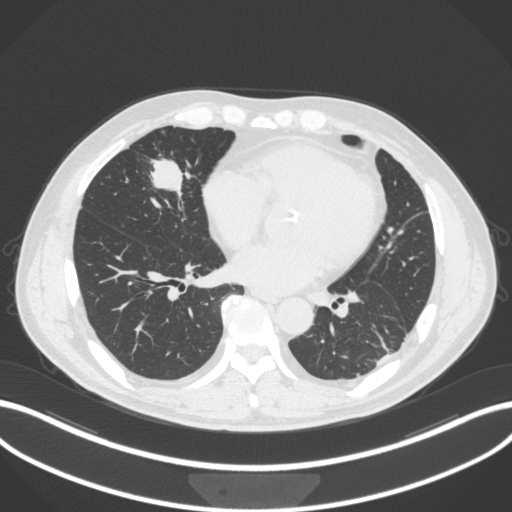
Chest CT, one axial slice; position 112 of 399 along the scan axis; 120 kVp; lung window (W 1500 / L -600 HU); 512 × 512 image matrix, field of view 400 × 400 mm. Male patient, age 59 years. Case-level facts recorded for this patient, not image findings: clinical TNM (as recorded): T2a N1 M0.
Structures marked on this image (bounding box drawn by a radiologist):
- lung tumour (recorded histology: adenocarcinoma): bounding box (x1, y1, x2, y2) in pixels: (144, 153, 191, 196)